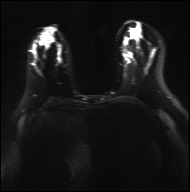
Breast MRI, one axial slice; position 15 of 36 along the scan axis; diffusion-weighted series; image 2 of 4 stored at this slice position (different b-values; order by instance number); 3 T; 4 mm slice thickness; 190 × 192 image matrix, field of view 317 × 320 mm. Female patient.
Outlined on this slice (outlined manually by an expert reader):
- tumour on diffusion-weighted imaging: bounding box <63,28,82,36> (left, top, right, bottom; pixels)